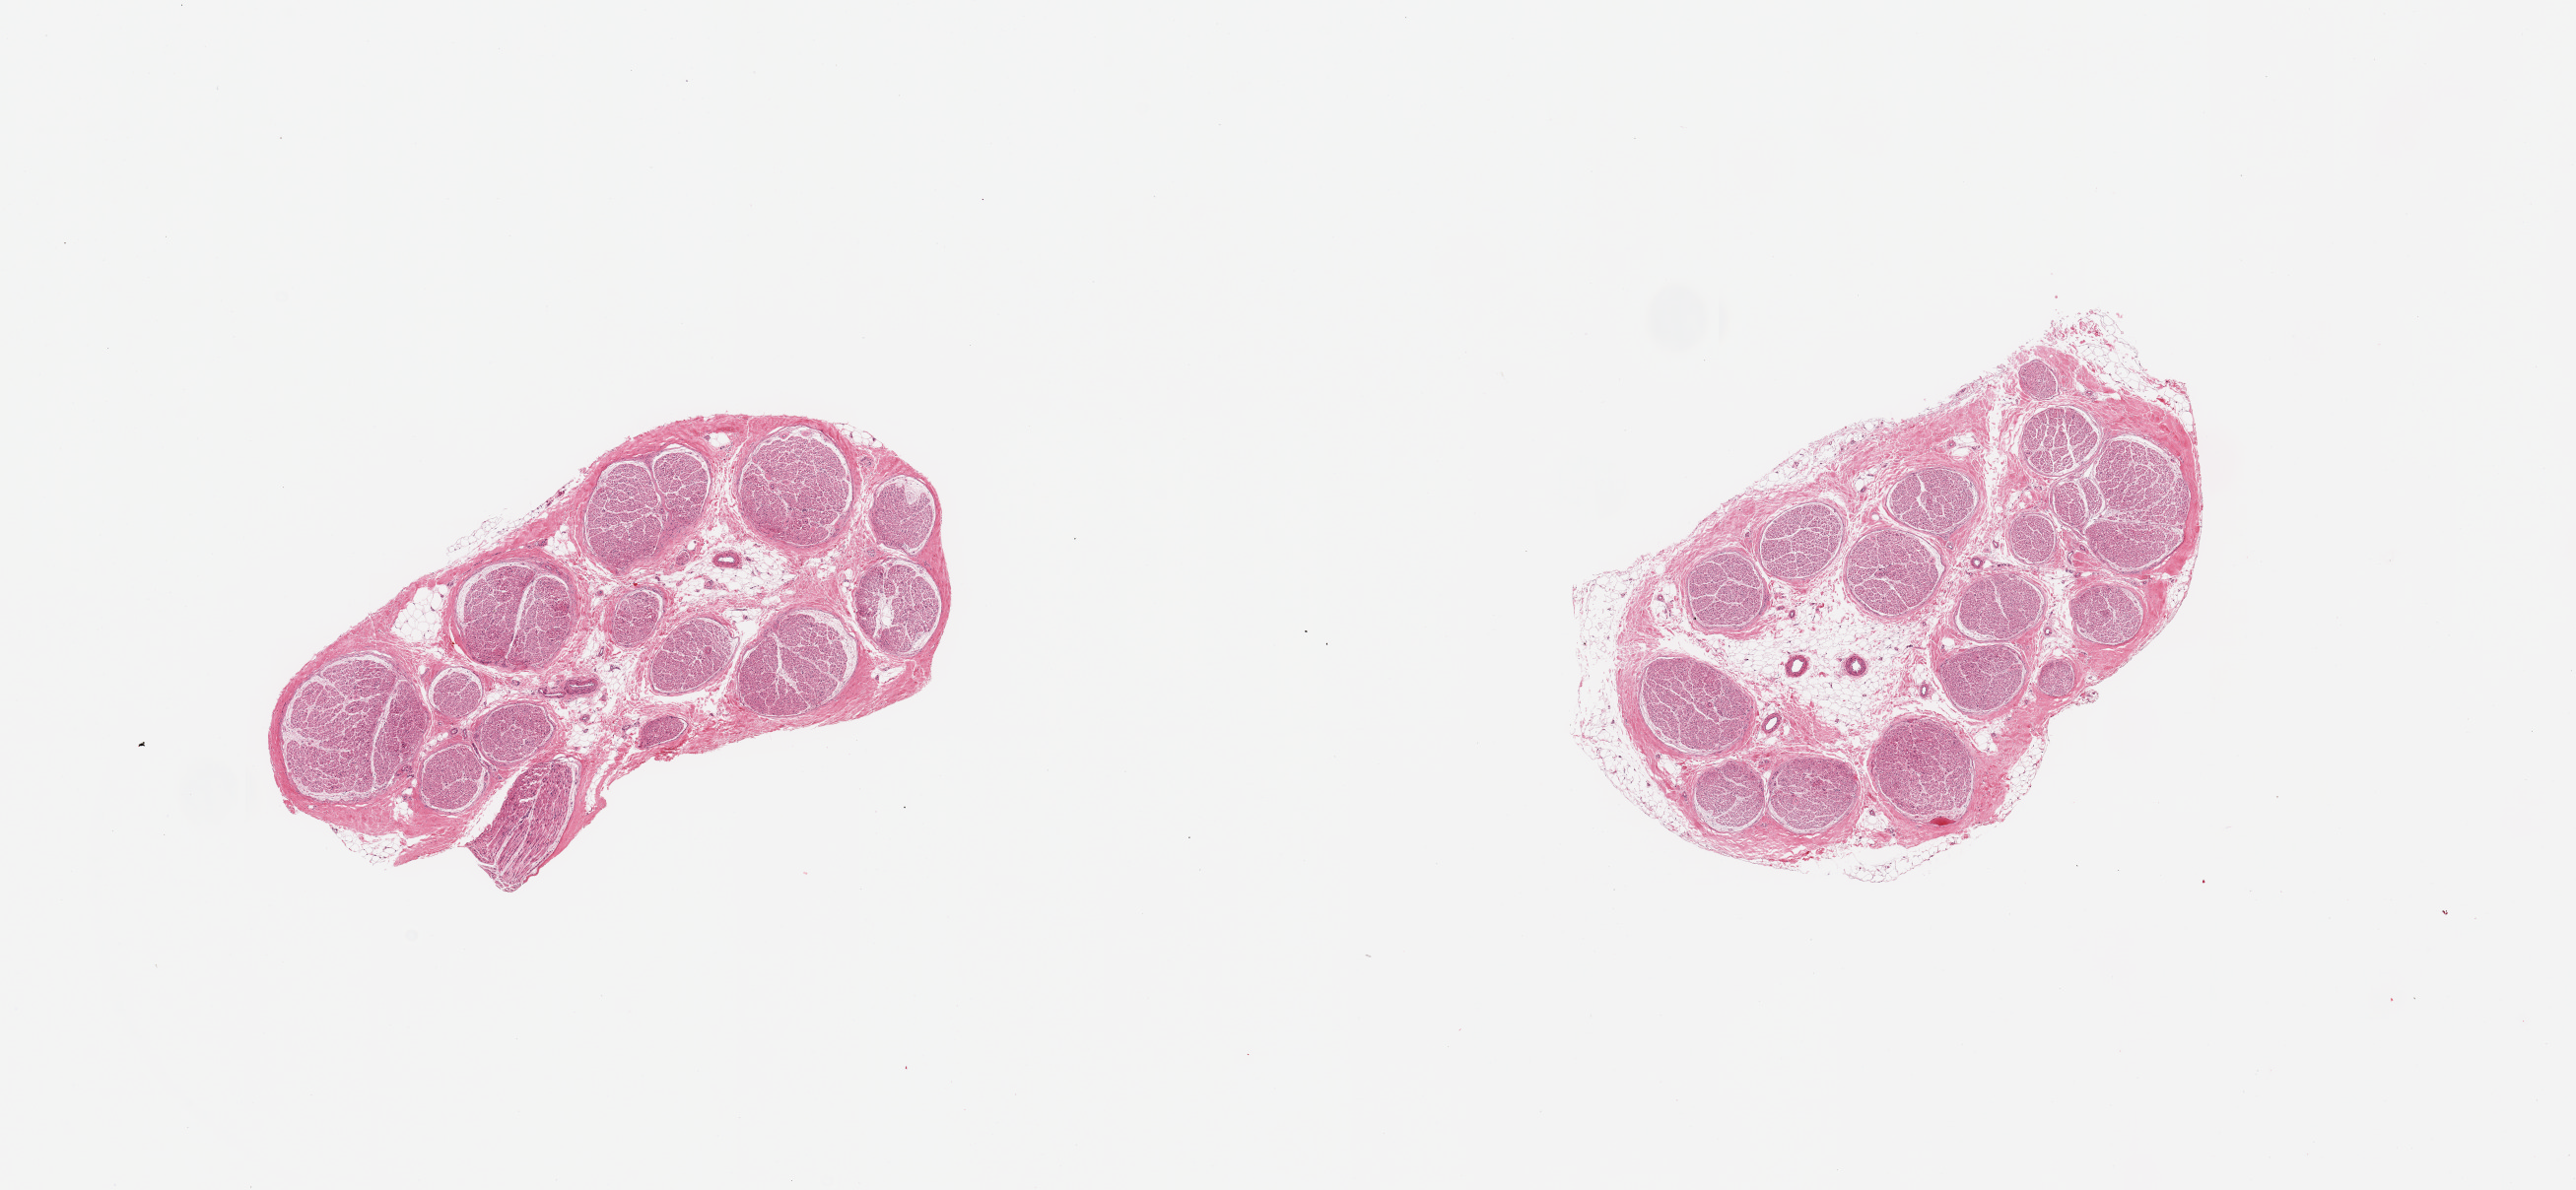
Digitized H&E-stained section — a low-resolution overview of the entire scanned area, about 20.7 x 9.6 mm (from a 20x scan); PAXgene-fixed, paraffin-embedded tissue; target tissue: tibial nerve; tissue donor sample. Donor sex: male.
Reviewer comment on this tissue sample: 2 pieces; well trimmed nerve with 20% internal fat.